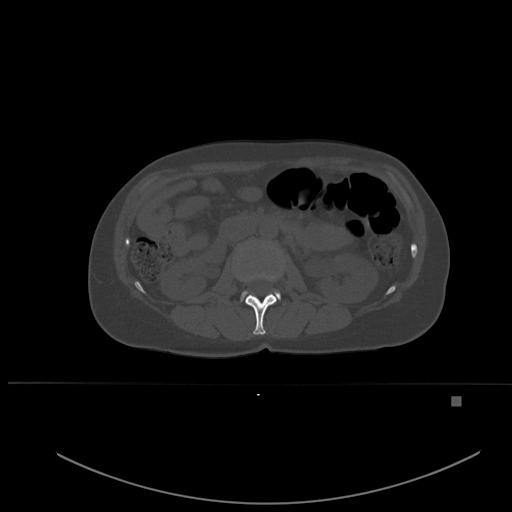
CT including the spine, one axial slice; position 225 of 651 along the scan axis; bone window (W 1800 / L 400 HU); 512 × 512 image matrix, field of view 443 × 443 mm. Patient: female, 49 years. Case-level facts recorded for this patient, not image findings: primary cancer: breast.
Outlined on this slice (semi-automatic segmentation, software-assisted and operator-edited):
- L1 vertebra: bounding box [x1, y1, x2, y2] px = [246, 274, 277, 335]
- L2 vertebra: [241, 291, 281, 301]